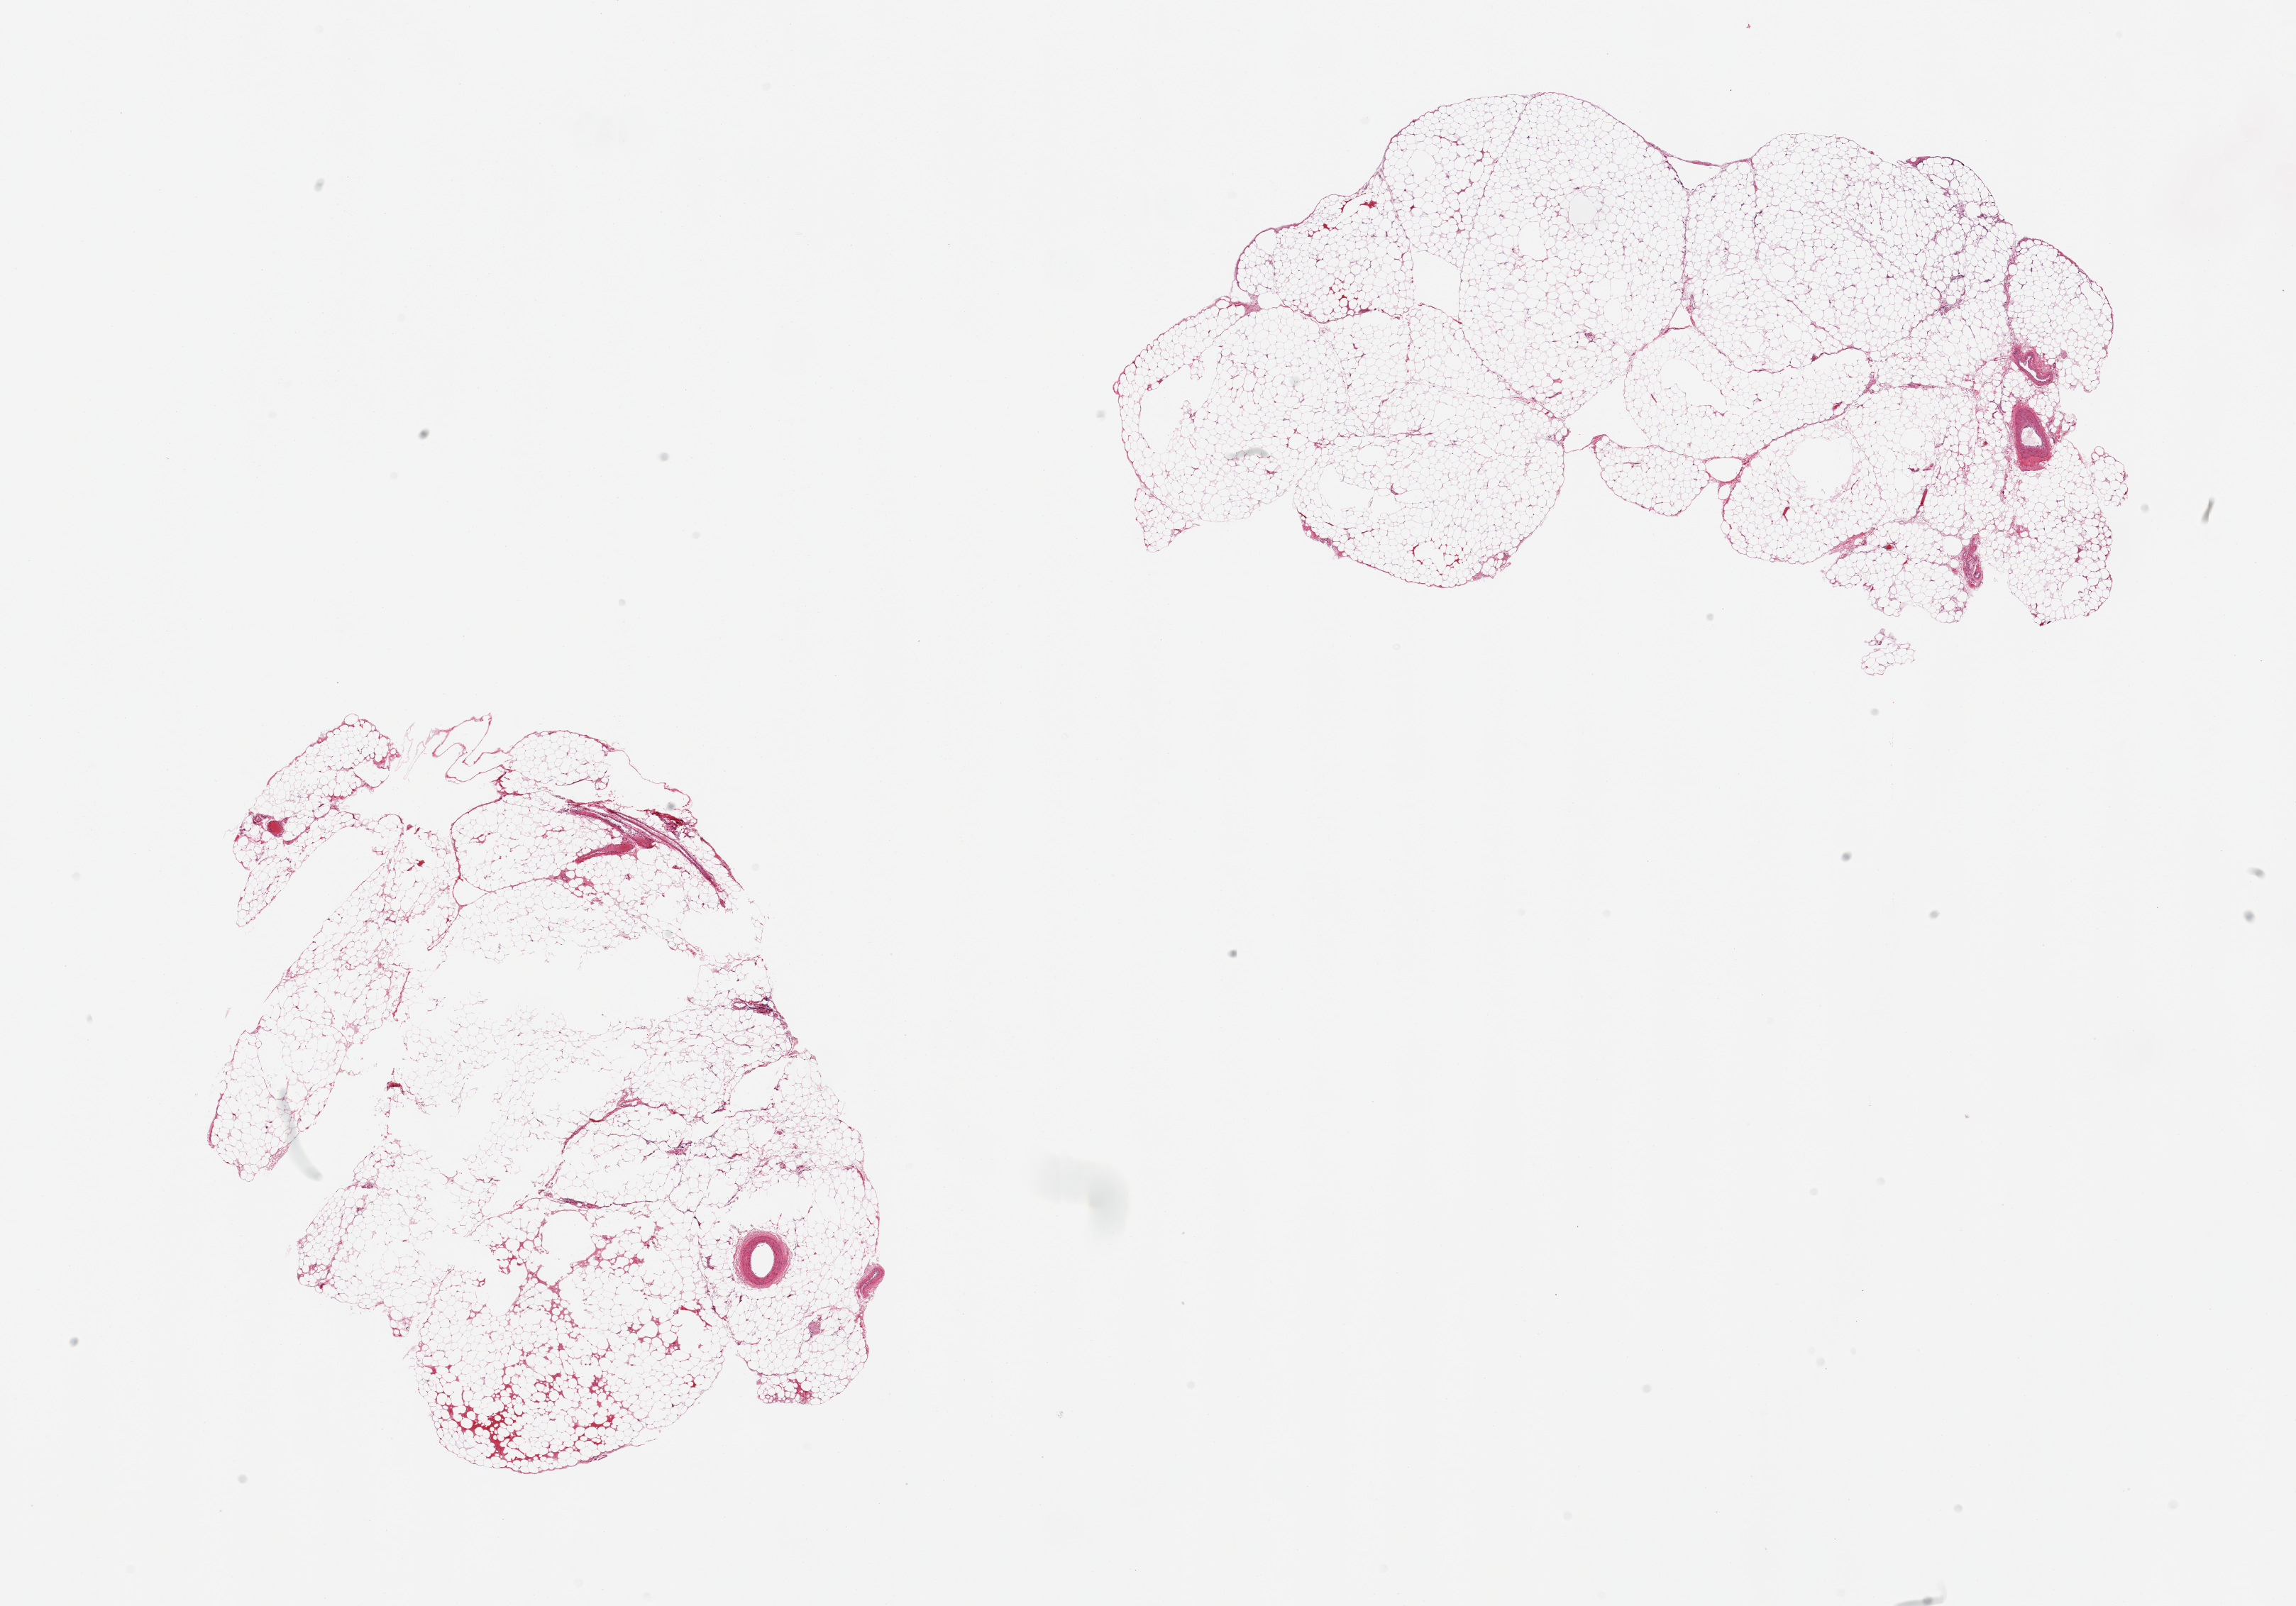
Whole-slide image, H&E stain — whole scanned area (about 25.6 x 17.9 mm, slide scanned at 20x) shown as a low-resolution overview. PAXgene-fixed paraffin-embedded (PFPE) section. Sampled site (target tissue): omentum. Tissue donor sample.
* reviewer comment on this tissue sample: 2 pieces